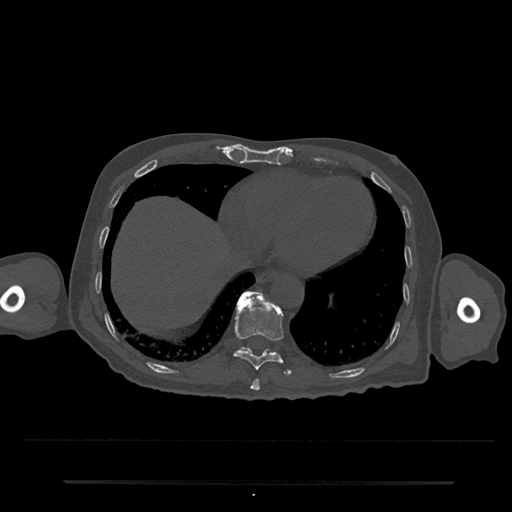
CT including the spine, one axial slice. Slice 306 of 797 in the series (ordered by position). Reconstruction kernel Br40s/3. 120 kVp. Bone window (W 1800 / L 400 HU). 512 × 512 image matrix. Patient: male, 74 years. Case-level facts recorded for this patient, not image findings: primary cancer: prostate.
Annotated regions visible in this slice (semi-automatic segmentation, software-assisted and operator-edited):
- T10 vertebra: bounding box <233,292,292,376> (left, top, right, bottom; pixels)
- T11 vertebra: <240,291,262,350>
- T9 vertebra: <250,379,260,391>